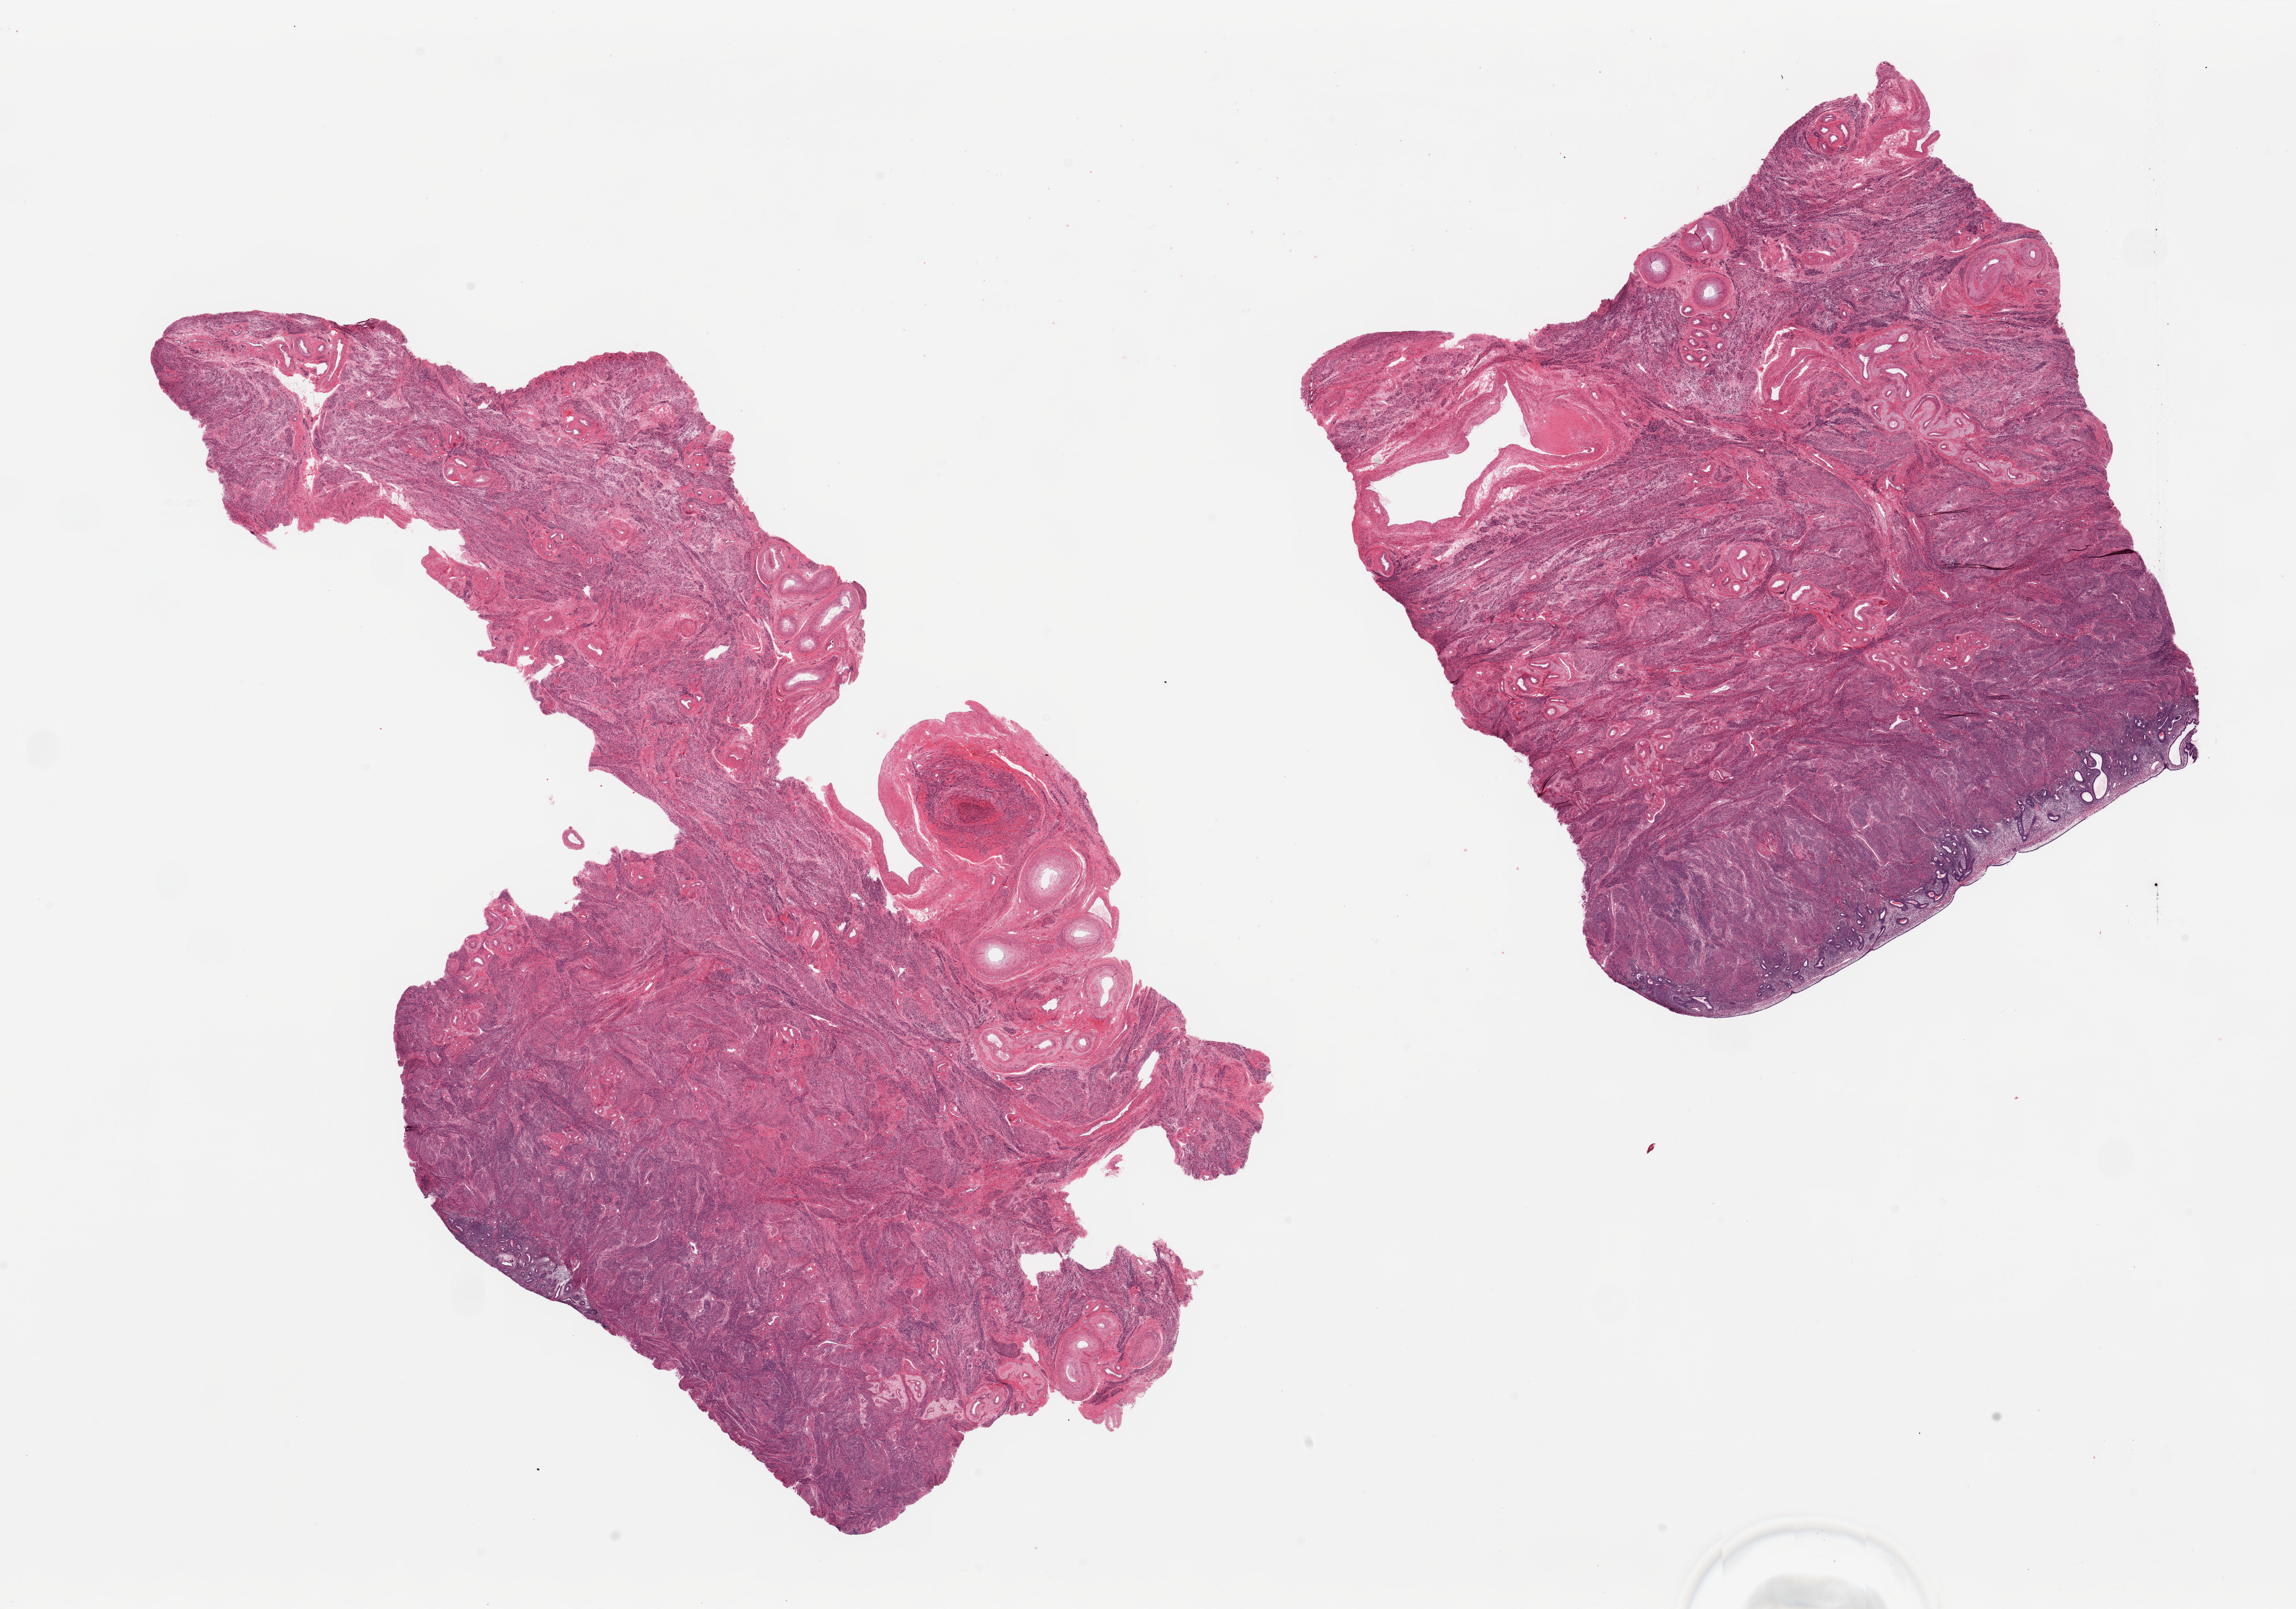
Whole-slide image, H&E stain, low-resolution overview of the scanned area, about 31.5 x 22.1 mm (from a 20x scan). PAXgene-fixed, paraffin-embedded tissue. Section of uterus (target tissue). Tissue donor sample.
Reviewer comment on this tissue sample: 2 pieces, ~0.5mm layer of inactive endometrium.